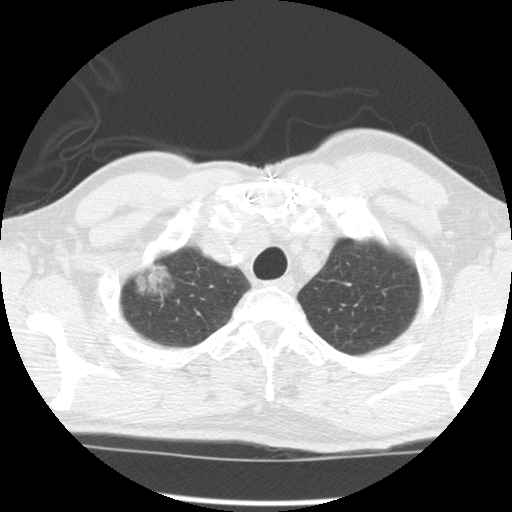
Chest CT (low-dose screening protocol), one axial image, second screening round (one year after baseline), lung window (W 1500 / L -600 HU), standard (soft-tissue) reconstruction kernel (STANDARD), 512 × 512 image matrix, field of view 340 × 340 mm. Male, age 64 years at enrolment. Former smoker at enrolment.
Lesion marked by an expert reader, box from (x=122, y=242) to (x=182, y=309) px. The screening reader recorded 2 non-calcified nodules or masses ≥4 mm on this exam; which of them this box marks is not recorded. Lung cancer was diagnosed 429 days after this screen: adenocarcinoma, NOS, right upper lobe, well differentiated (G1), stage IB (AJCC 6th edition), 45 mm at pathology.